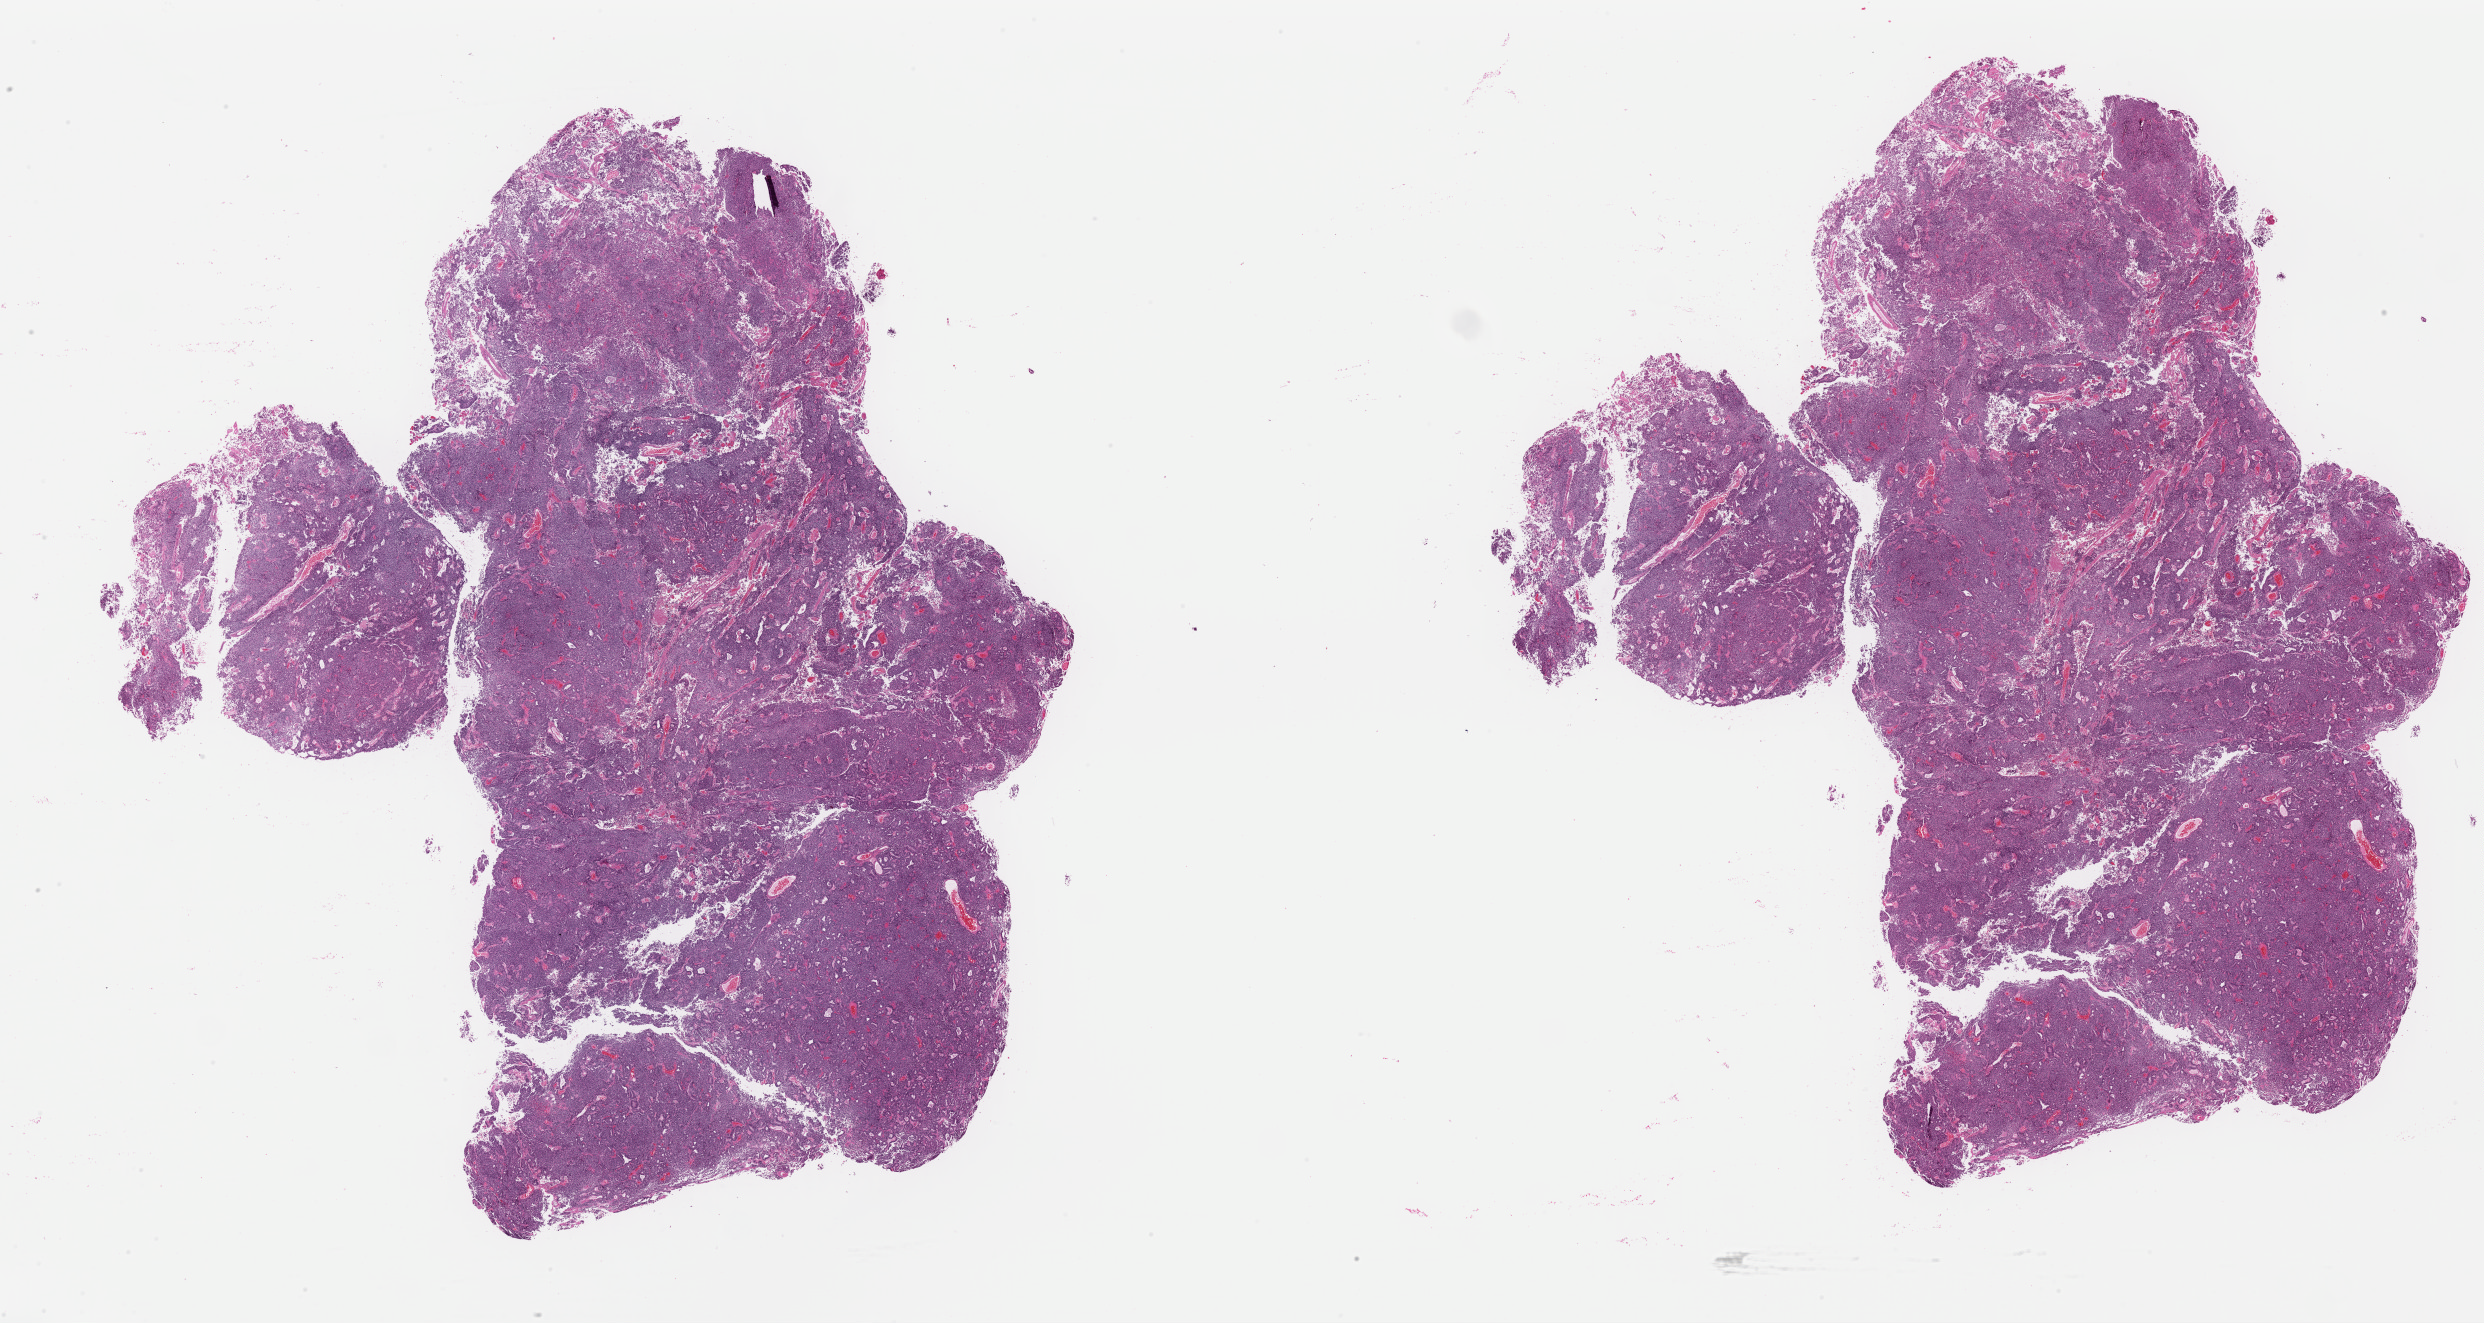
Digitized H&E-stained tissue section (whole slide) — a low-resolution overview of the entire scanned area, about 39.2 x 20.9 mm (from a 40x scan); formalin-fixed paraffin-embedded (FFPE) diagnostic section; primary tumour sample from the uterus. Female patient; age at initial diagnosis 76 years. Histologic grade: G2 (moderately differentiated).
Histologic diagnosis: Endometrioid adenocarcinoma, NOS. FIGO stage: IIIA.